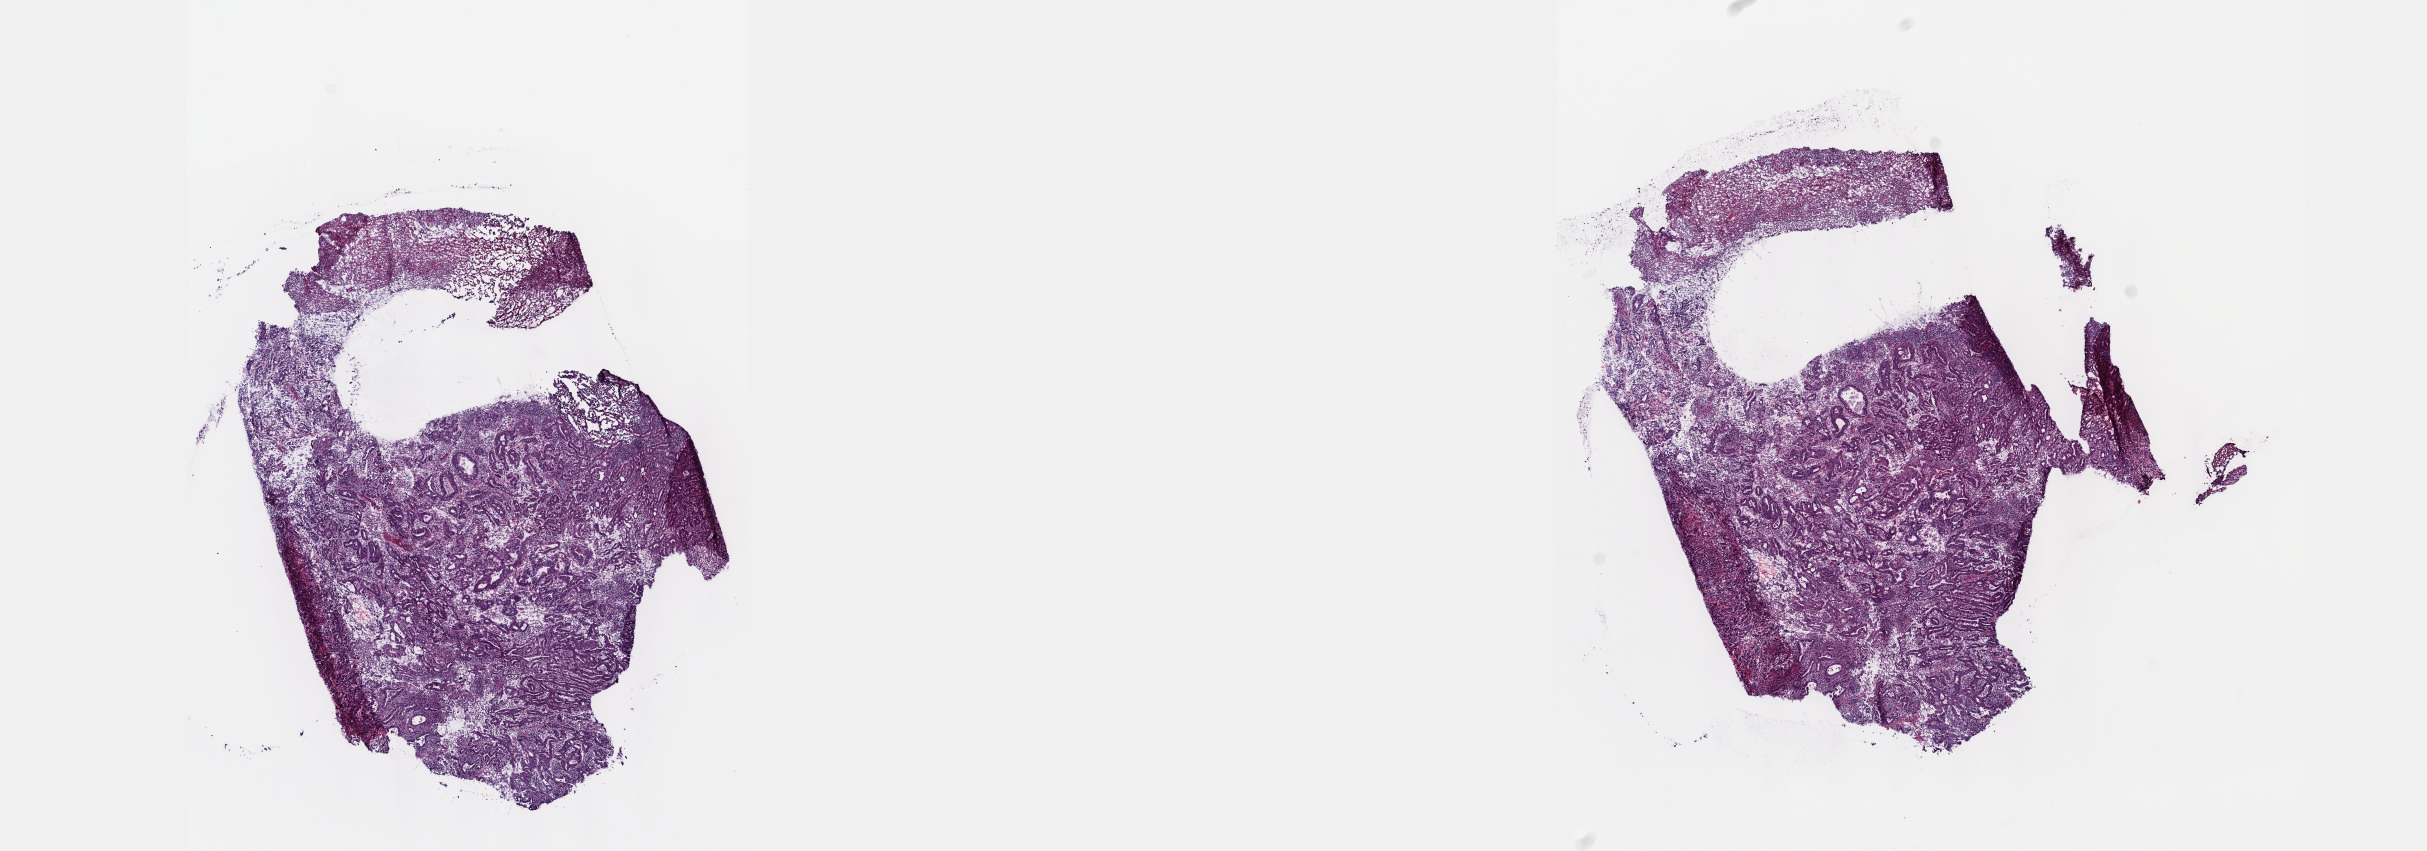
Digitized H&E-stained tissue section (whole slide) — whole scanned area (about 19.6 x 6.9 mm, from a 40x scan) shown as a low-resolution overview; frozen section from the top of the tissue portion; primary tumour sample from the stomach. Male patient; age at initial diagnosis 56 years. Histologic grade: G3 (poorly differentiated). Pathologist review of this section (percent, as recorded): tumour cells 100%, tumour nuclei 65%, normal cells 0%, stromal cells 0%, necrosis 0%. Infiltration values recorded for this section: lymphocyte infiltration 5%, monocyte infiltration 0%, neutrophil infiltration 0%.
- histologic diagnosis: Adenocarcinoma, intestinal type
- AJCC pathologic stage: IIIB (6th edition)
- lymph nodes positive (case pathology): 9 of 17 examined